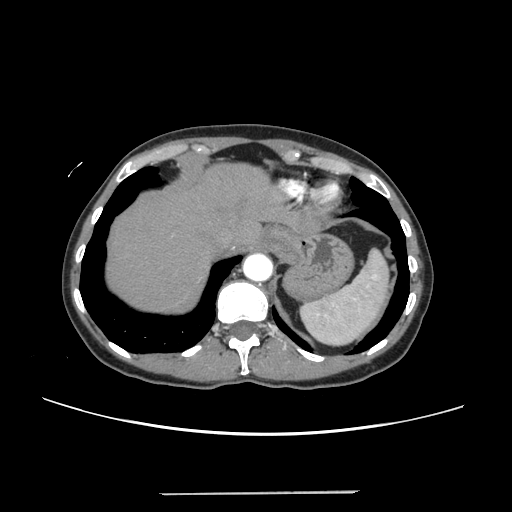
Contrast-enhanced abdominal CT, one axial slice. Position 207 of 240 along the scan axis. 120 kVp. Soft-tissue window (W 400 / L 40 HU). 512 × 512 image matrix, field of view 371 × 371 mm. Female patient, age 60 years. Case-level facts recorded for this patient, not image findings: diagnosis: colorectal cancer liver metastases, imaged before liver resection; multiple liver metastases: no; largest metastasis: 1.5 cm; chemotherapy before resection: yes.
Annotated regions visible in this slice (manually delineated by an expert):
- hepatic veins: bounding box <221,224,250,243> (left, top, right, bottom; pixels)
- liver: <107,164,304,312>
- planned liver remnant (the part of the liver to remain after resection): <107,164,303,312>